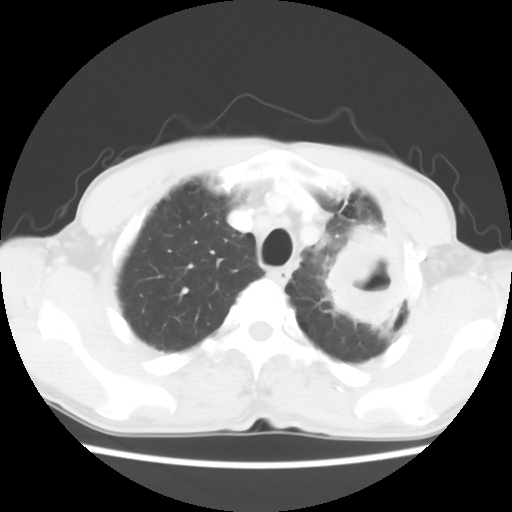
Chest CT, one axial slice; position 49 of 60 along the scan axis; lung window (W 1500 / L -600 HU); 512 × 512 image matrix, field of view 308 × 308 mm. Patient: male, 64 years. Case-level facts recorded for this patient, not image findings: clinical TNM (as recorded): T3 N3 M0; histopathological grade: G3.
Outlined on this slice (rectangle marked by the reading radiologist):
- lung tumour (recorded histology: adenocarcinoma): bounding box <316,223,411,343> (left, top, right, bottom; pixels)